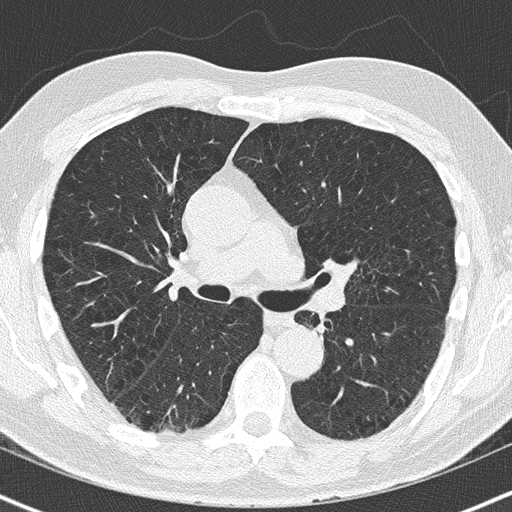
Low-dose screening chest CT, one axial slice; reconstruction kernel B50f; 120 kVp; lung window (W 1500 / L -600 HU); 512 × 512 image matrix.
Outlined on this slice (manually delineated by an expert):
- lesion 1 (tumor, upper lobe of left lung): bounding box (x1, y1, x2, y2) in pixels: (359, 261, 366, 262)